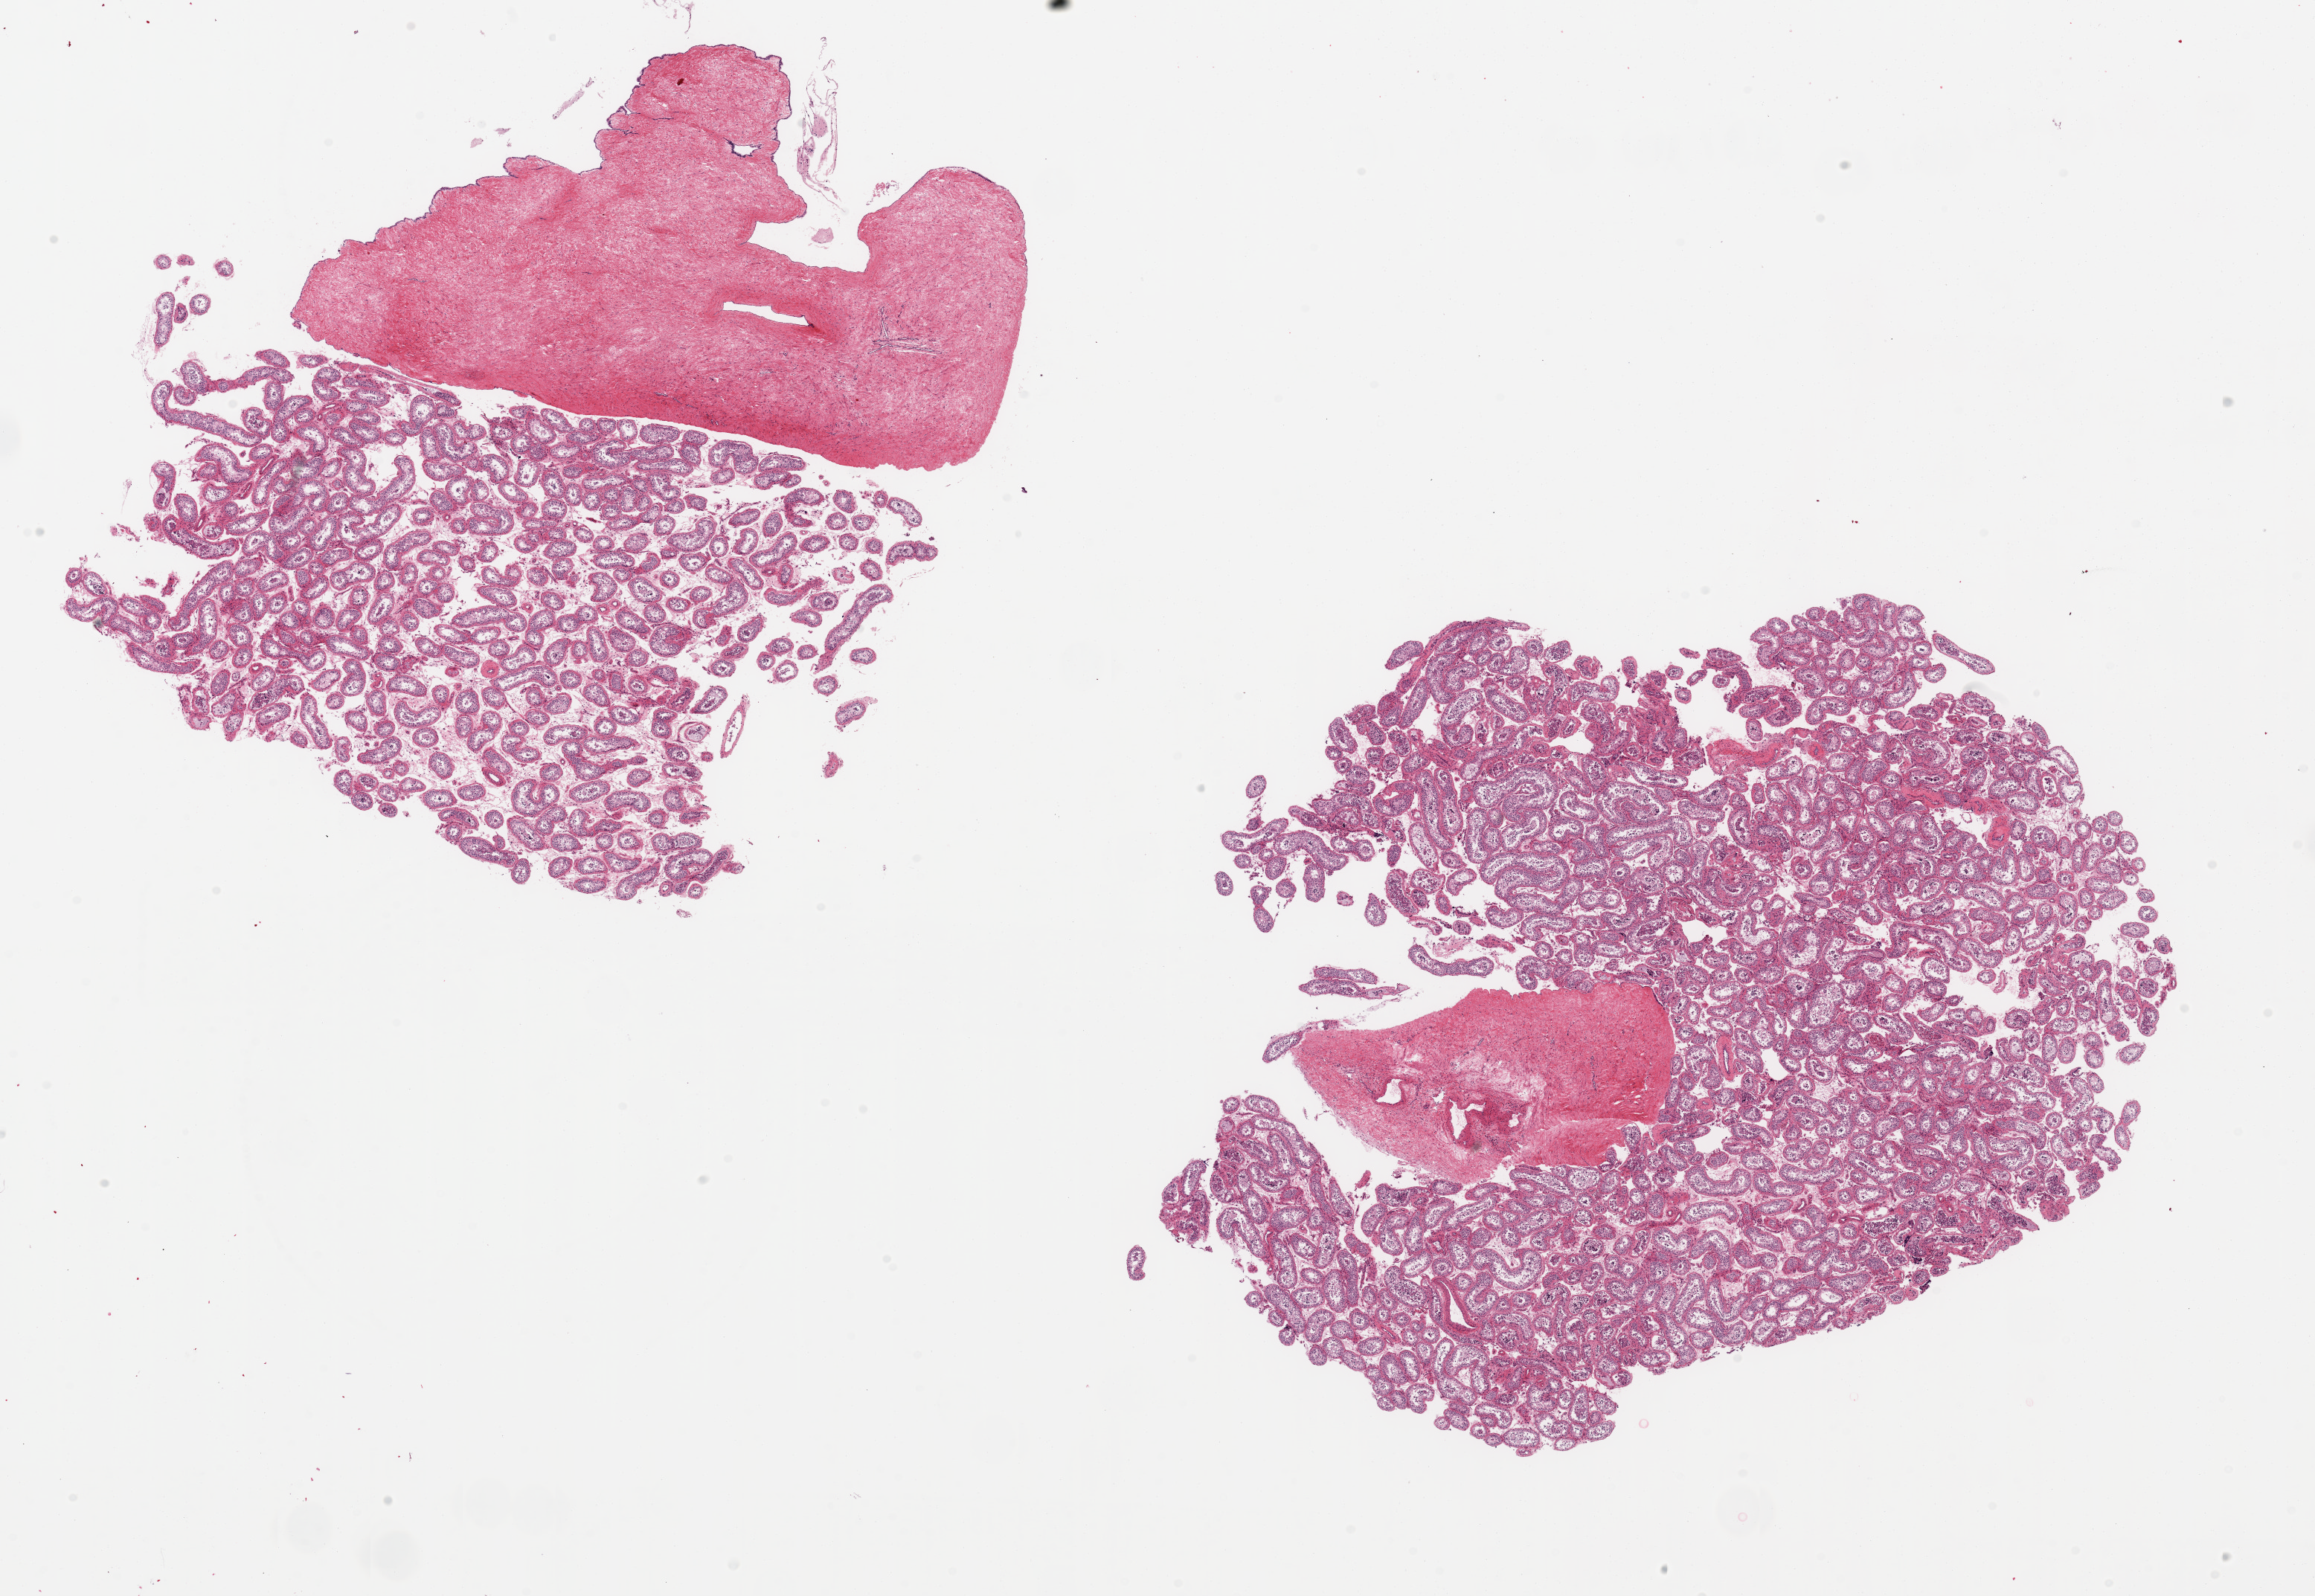
Whole-slide image, hematoxylin and eosin (H&E) stain, a low-resolution overview of the entire scanned area, about 24.6 x 17.0 mm; PAXgene-fixed paraffin-embedded (PFPE) section; target tissue: testis; tissue donor sample. Donor sex: male.
* pathologist's review note for this sample: 2 ~ 8 .56mm pieces, one with attached 7x4mm piece of fibrous tissue